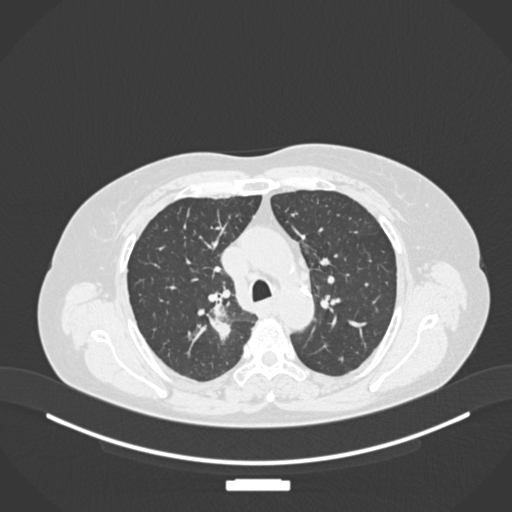
Chest CT, one axial slice; reconstruction kernel B30f; lung window (W 1500 / L -600 HU); 1 mm slice thickness; 512 × 512 image matrix, field of view 400 × 400 mm. Female patient, age 62 years. Case-level facts recorded for this patient, not image findings: clinical TNM (as recorded): T1c N1 M0.
Structures marked on this image (bounding box drawn by a radiologist):
- lung tumour (recorded histology: squamous cell carcinoma): box from (x=200, y=300) to (x=231, y=344) px